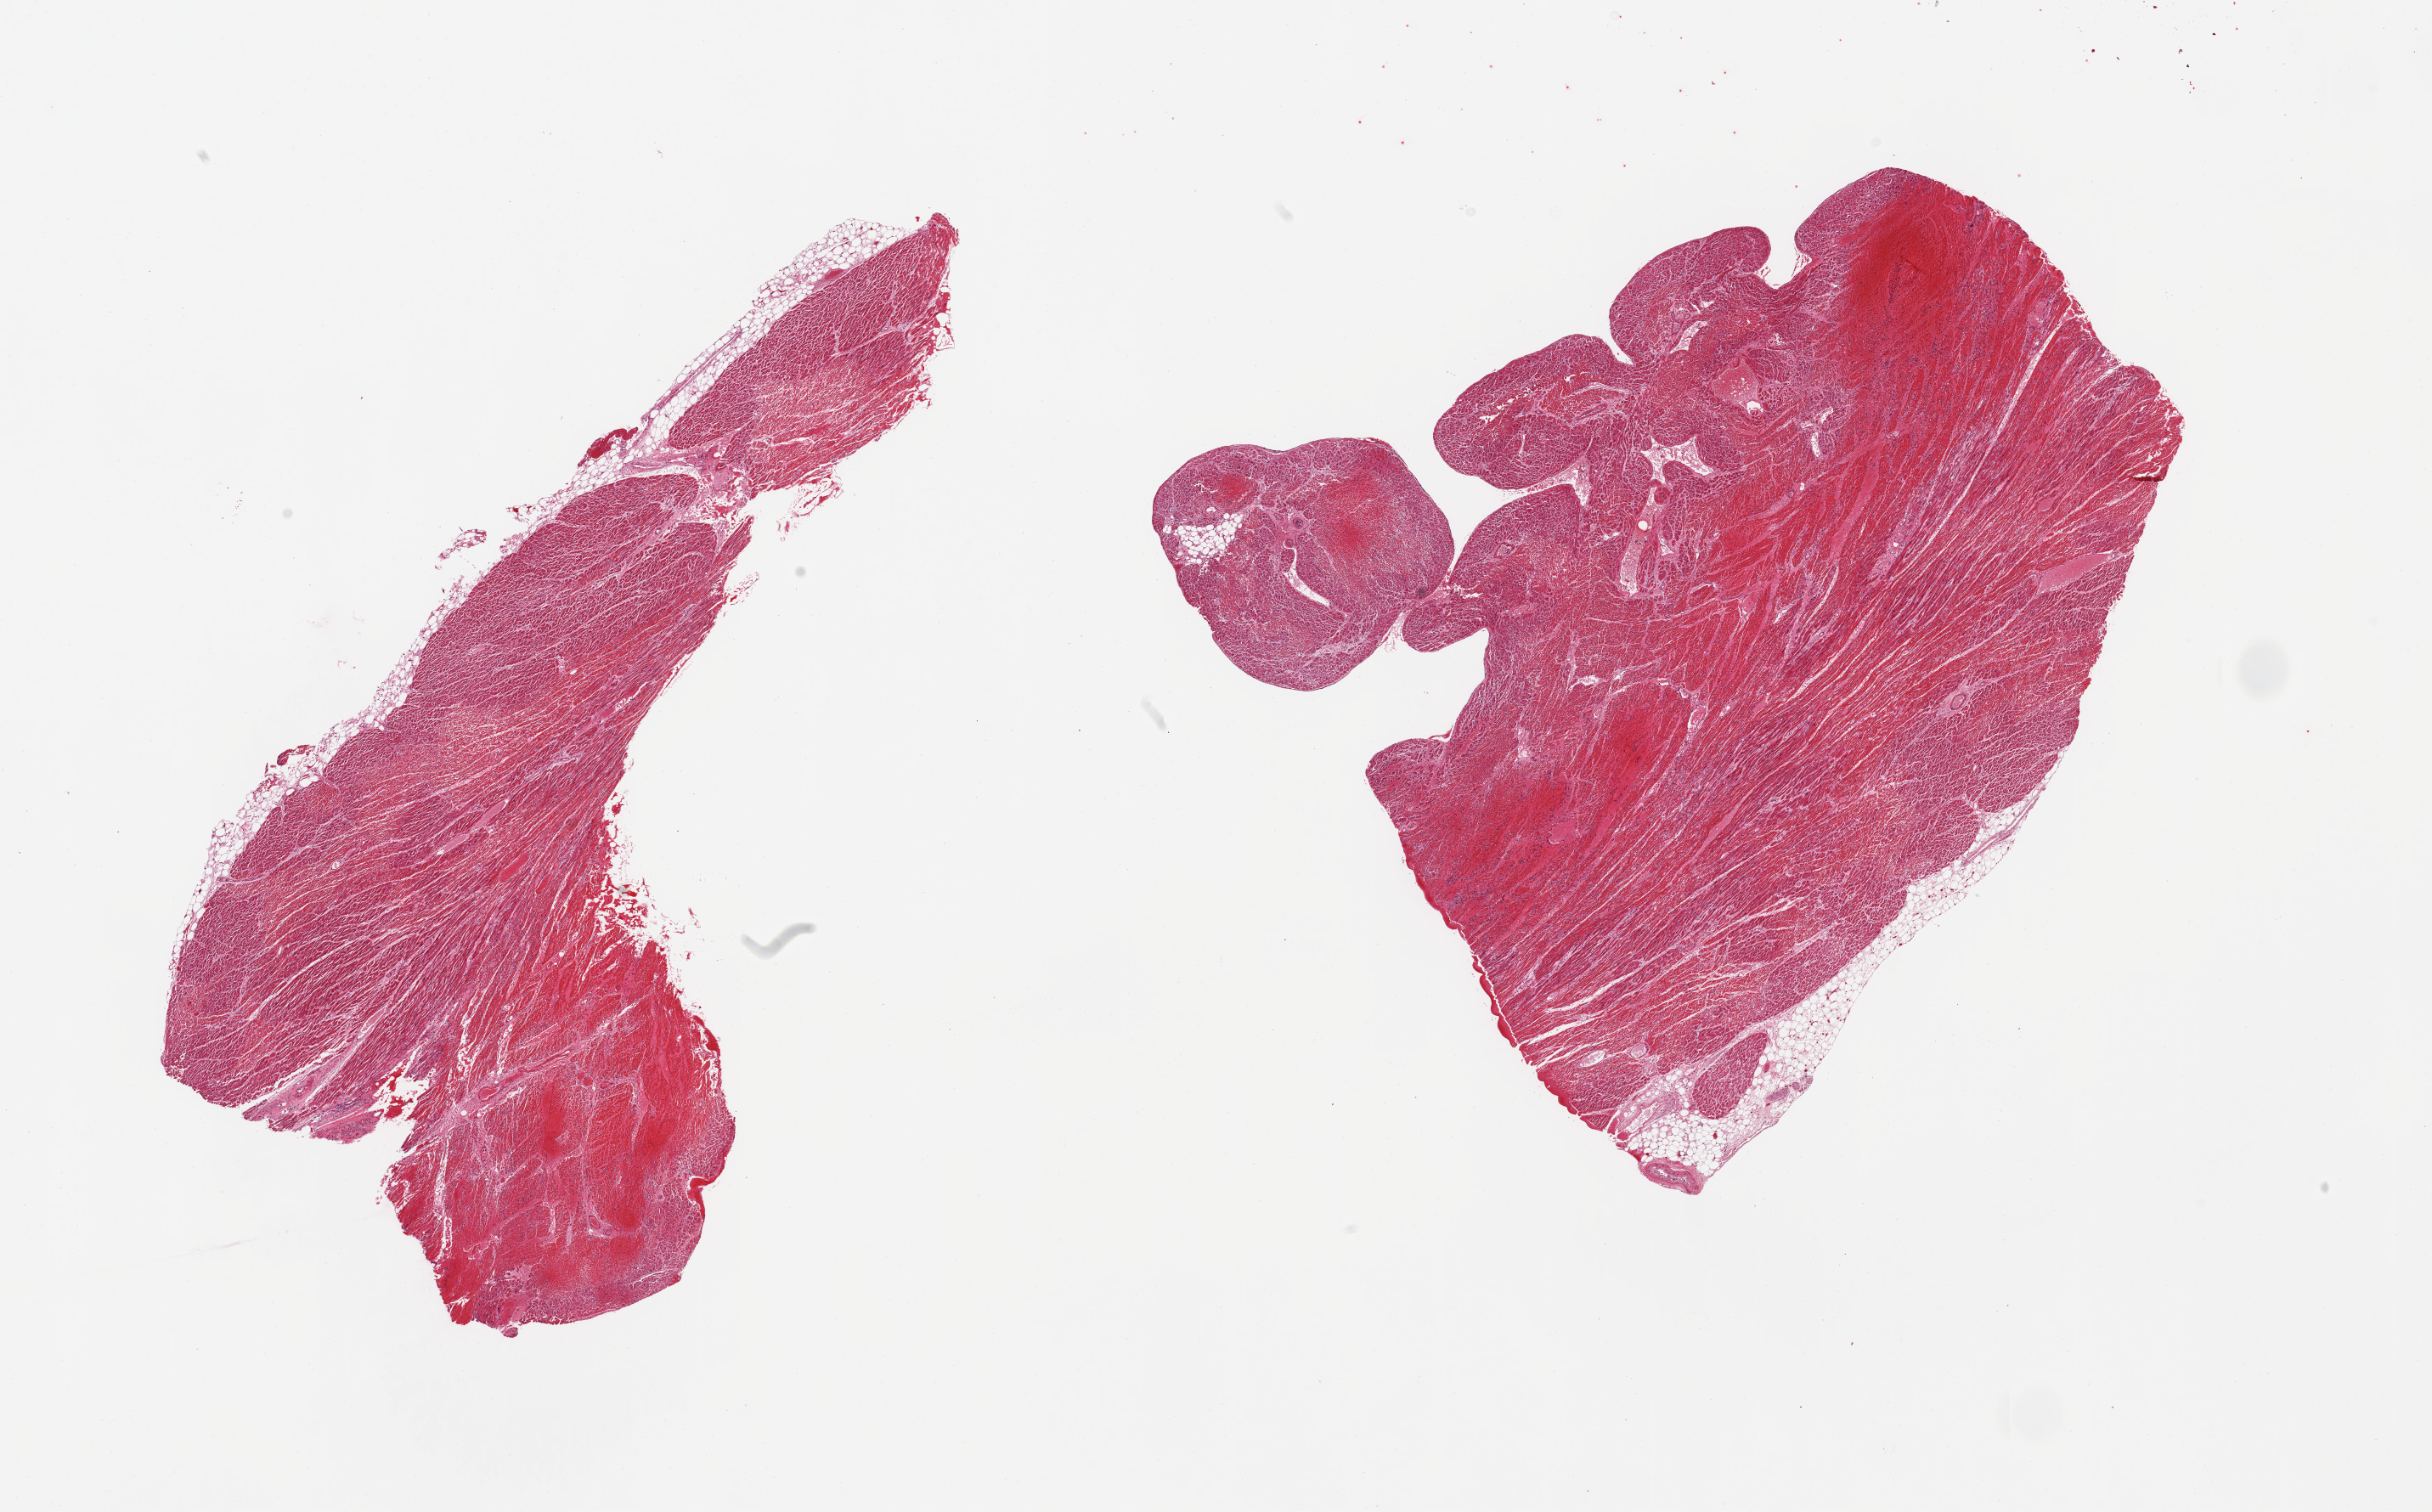
Whole-slide image, haematoxylin and eosin stain — low-resolution overview of the scanned area, about 22.6 x 14.1 mm (slide scanned at 20x), PAXgene-fixed paraffin-embedded (PFPE) section, target tissue: heart, donor tissue sample.
Pathologist's review note for this sample: 2 pieces; hemorrhagic infarct in both pieces, 30 & 20%.